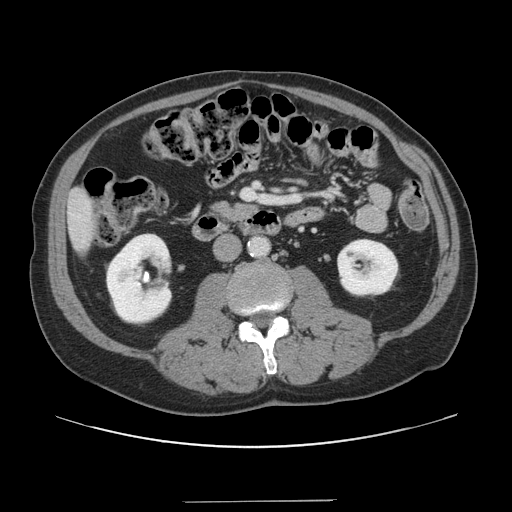
Contrast-enhanced abdominal CT, one axial slice. Slice 40 of 151 in the series (ordered by position). Intravenous contrast given. Soft-tissue window (W 400 / L 40 HU). 512 × 512 image matrix. Male patient, age 63 years. From the clinical record (not read from this slice): diagnosis: colorectal cancer liver metastases, imaged before liver resection; multiple liver metastases: no; largest metastasis: 2.1 cm; disease in both lobes: no.
Outlined on this slice (manually delineated by an expert):
- liver: box from (x=69, y=188) to (x=97, y=251) px
- planned liver remnant (the part of the liver to remain after resection): (x=69, y=188)–(x=97, y=251)
- portal vein (with intrahepatic branches): (x=242, y=189)–(x=278, y=202)